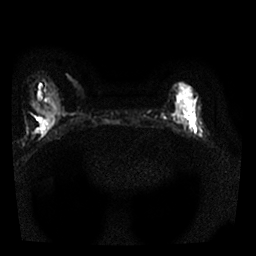
Breast MRI, one axial slice. Slice 8 of 25 in the series (ordered by position). Diffusion-weighted series; image 2 of 4 stored at this slice position (different b-values; order by instance number). 1.5 T. 4 mm slice thickness. 256 × 256 image matrix, field of view 300 × 300 mm. Female patient.
Structures marked on this image (expert manual segmentation):
- tumour on diffusion-weighted imaging: box from (x=188, y=116) to (x=193, y=122) px